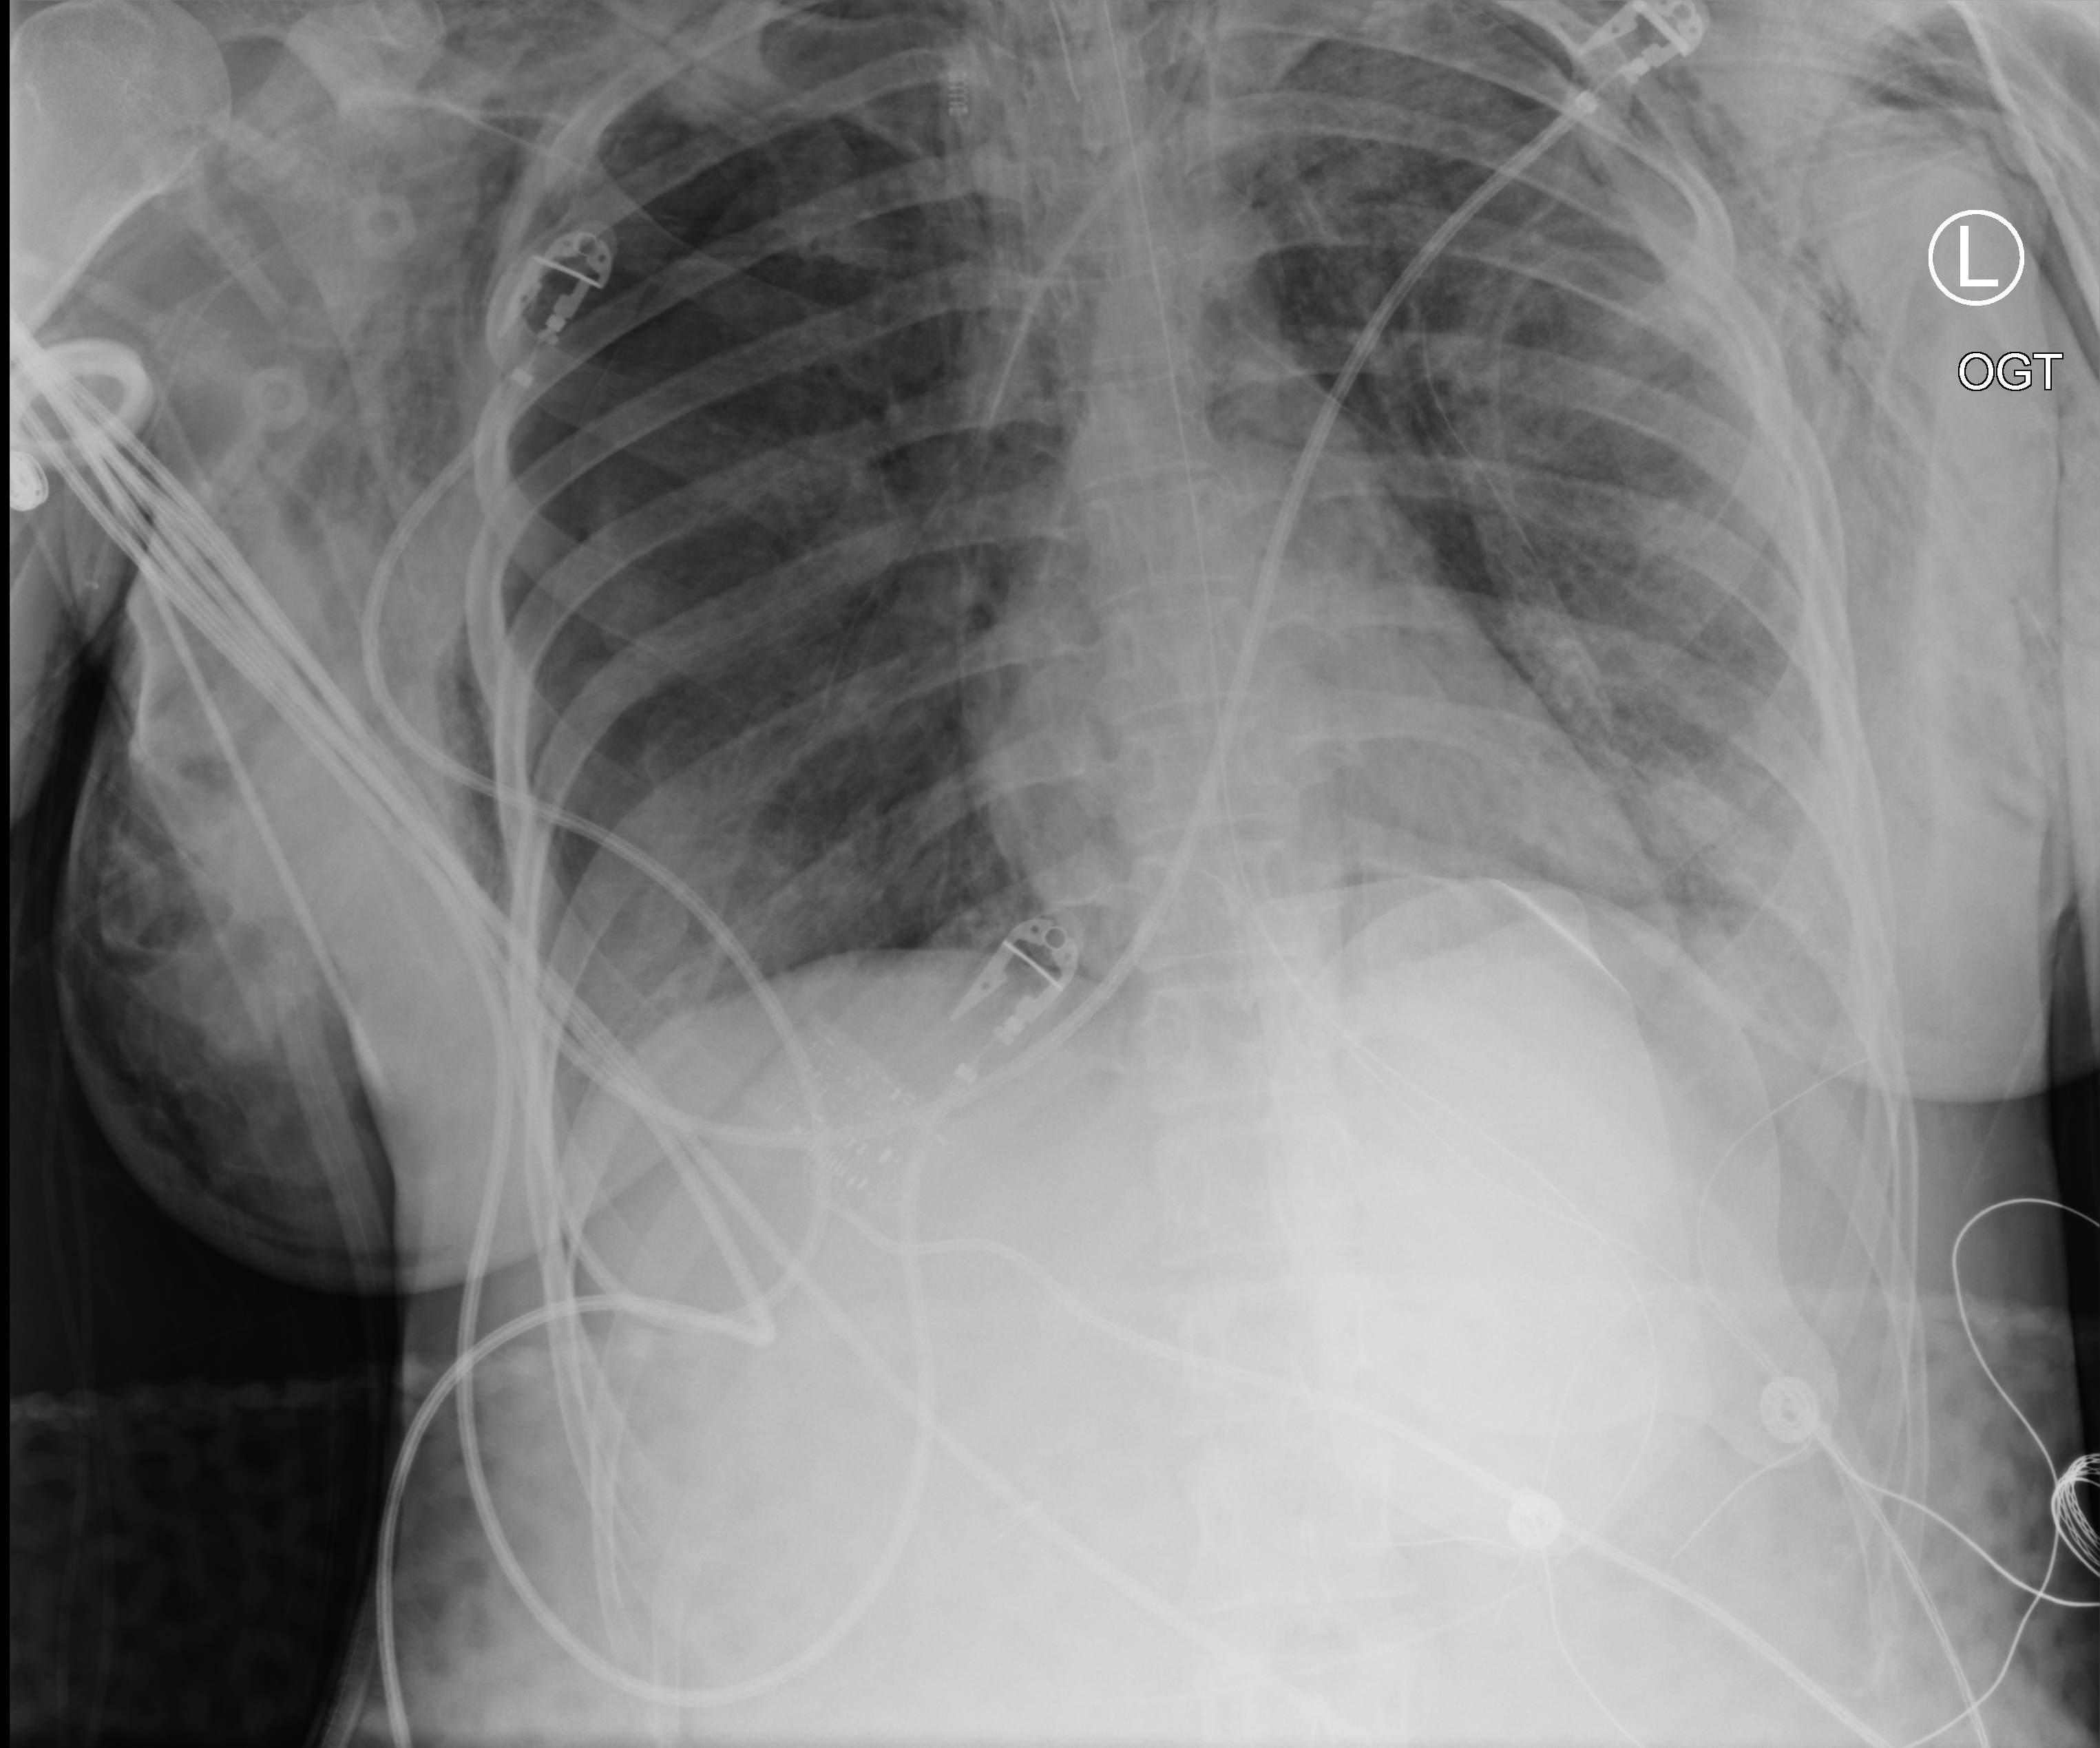
Chest X-ray (portable), anteroposterior (AP) projection. Patient hospitalised with COVID-19, aged 18–59 years.
Hospital-stay facts (about this admission, not read from this image; timing relative to this image not recorded):
- COPD (admission record): no
- admitted to intensive care during this hospital stay: yes
- mechanically ventilated during this hospital stay: yes